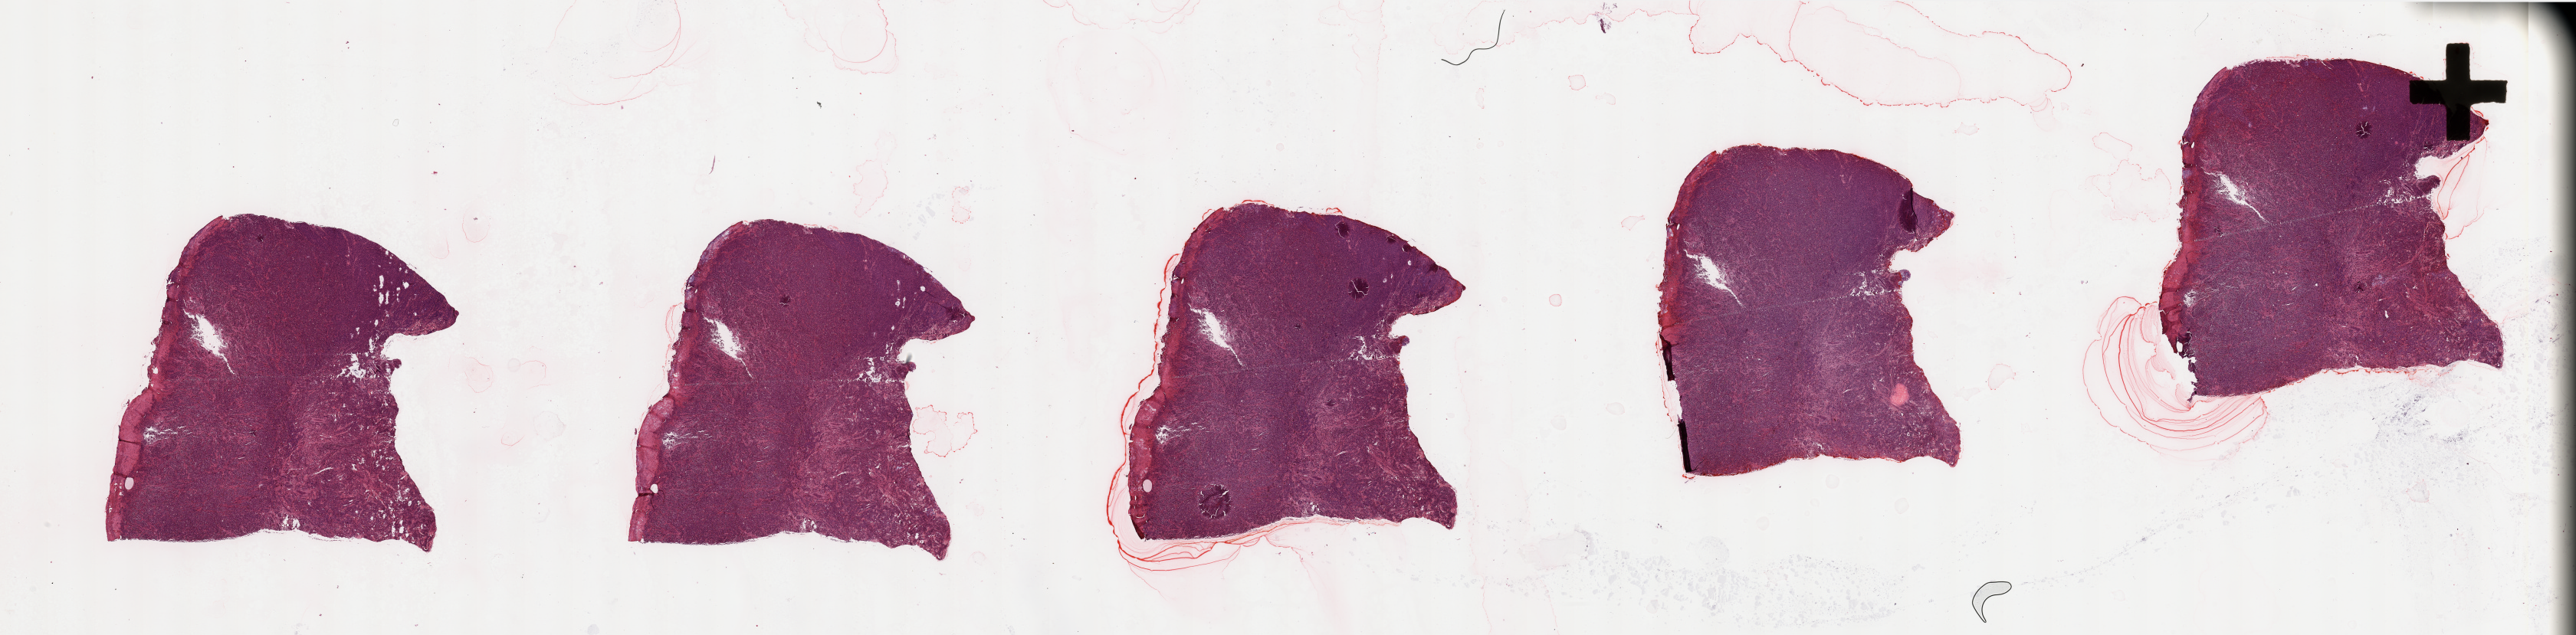
Hematoxylin and eosin (H&E) stained whole-slide image — whole scanned area (about 53.2 x 13.1 mm, acquisition: 20x scan) shown as a low-resolution overview, tumour tissue sample, sampled site: trunk. Patient: male, age 42 years. Composition of this section per pathologist review: tumour nuclei 95%, necrosis 0%.
Diagnosis: Malignant melanoma, NOS.